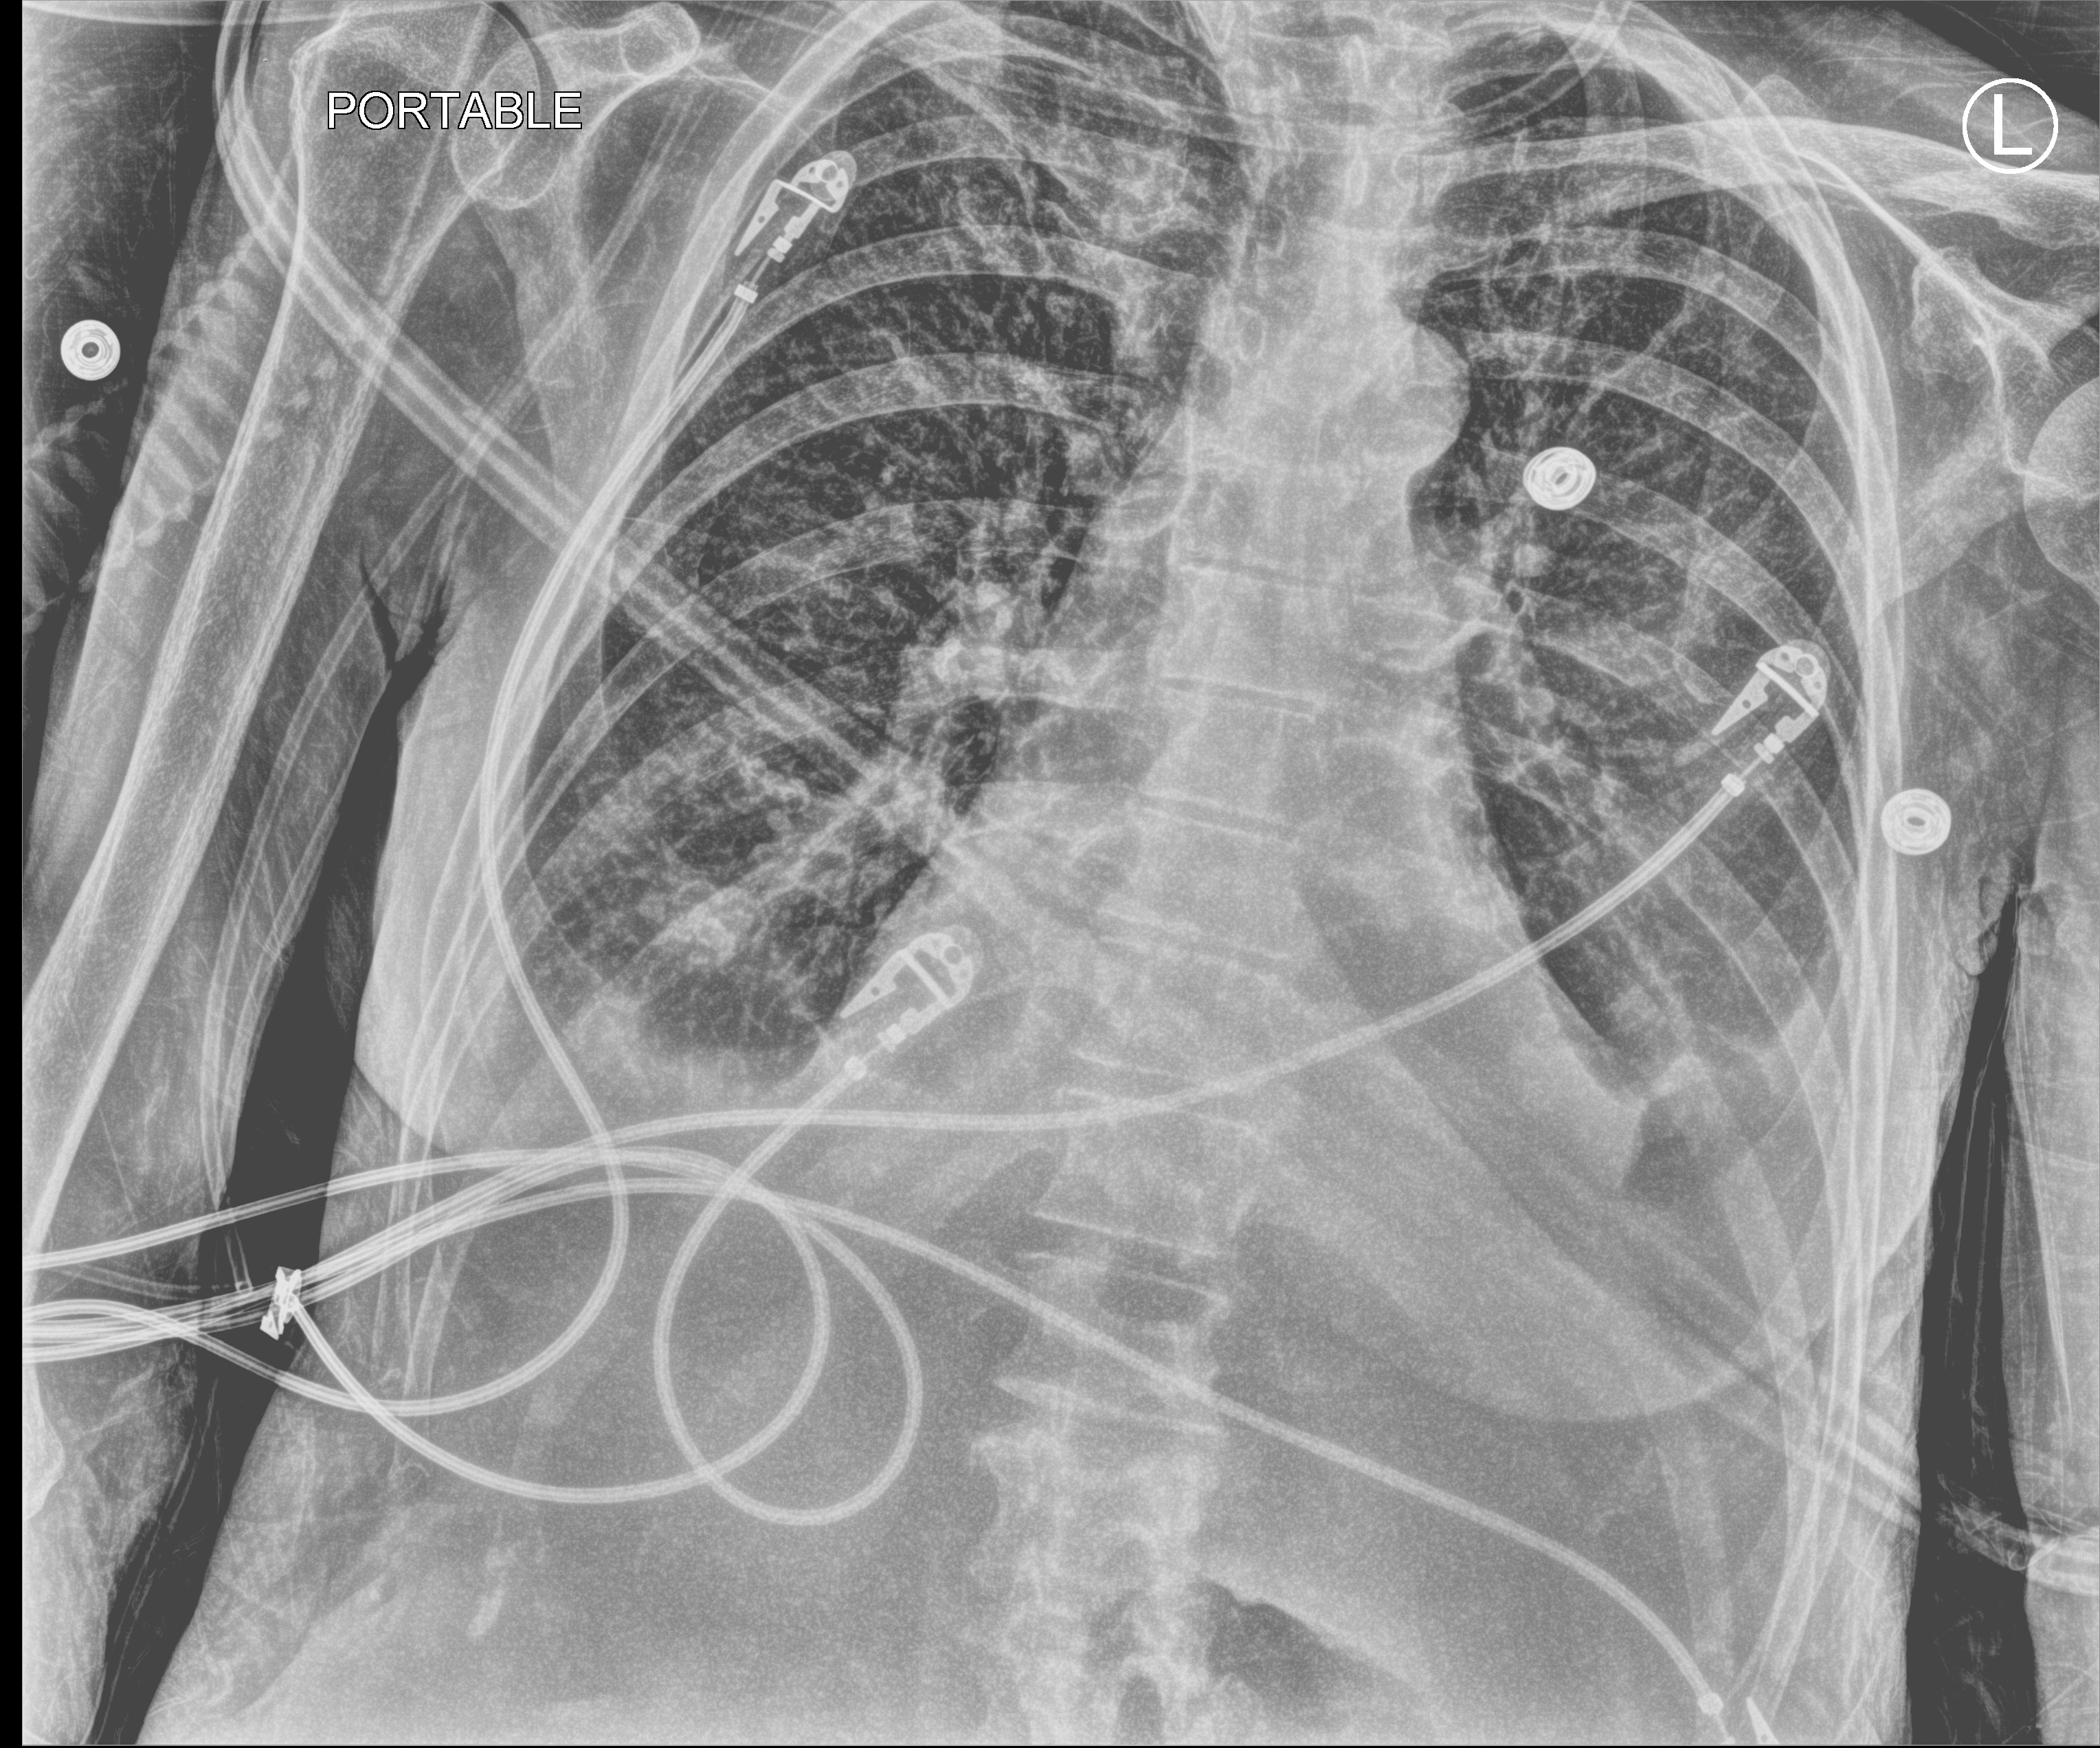
Portable chest radiograph, anteroposterior (AP) projection. Patient hospitalised with COVID-19; female, aged 60–74 years.
From the hospital-stay record, not from the radiograph (when in the stay this image was taken is not recorded):
- mechanically ventilated during this hospital stay: yes
- admitted to intensive care during this hospital stay: yes